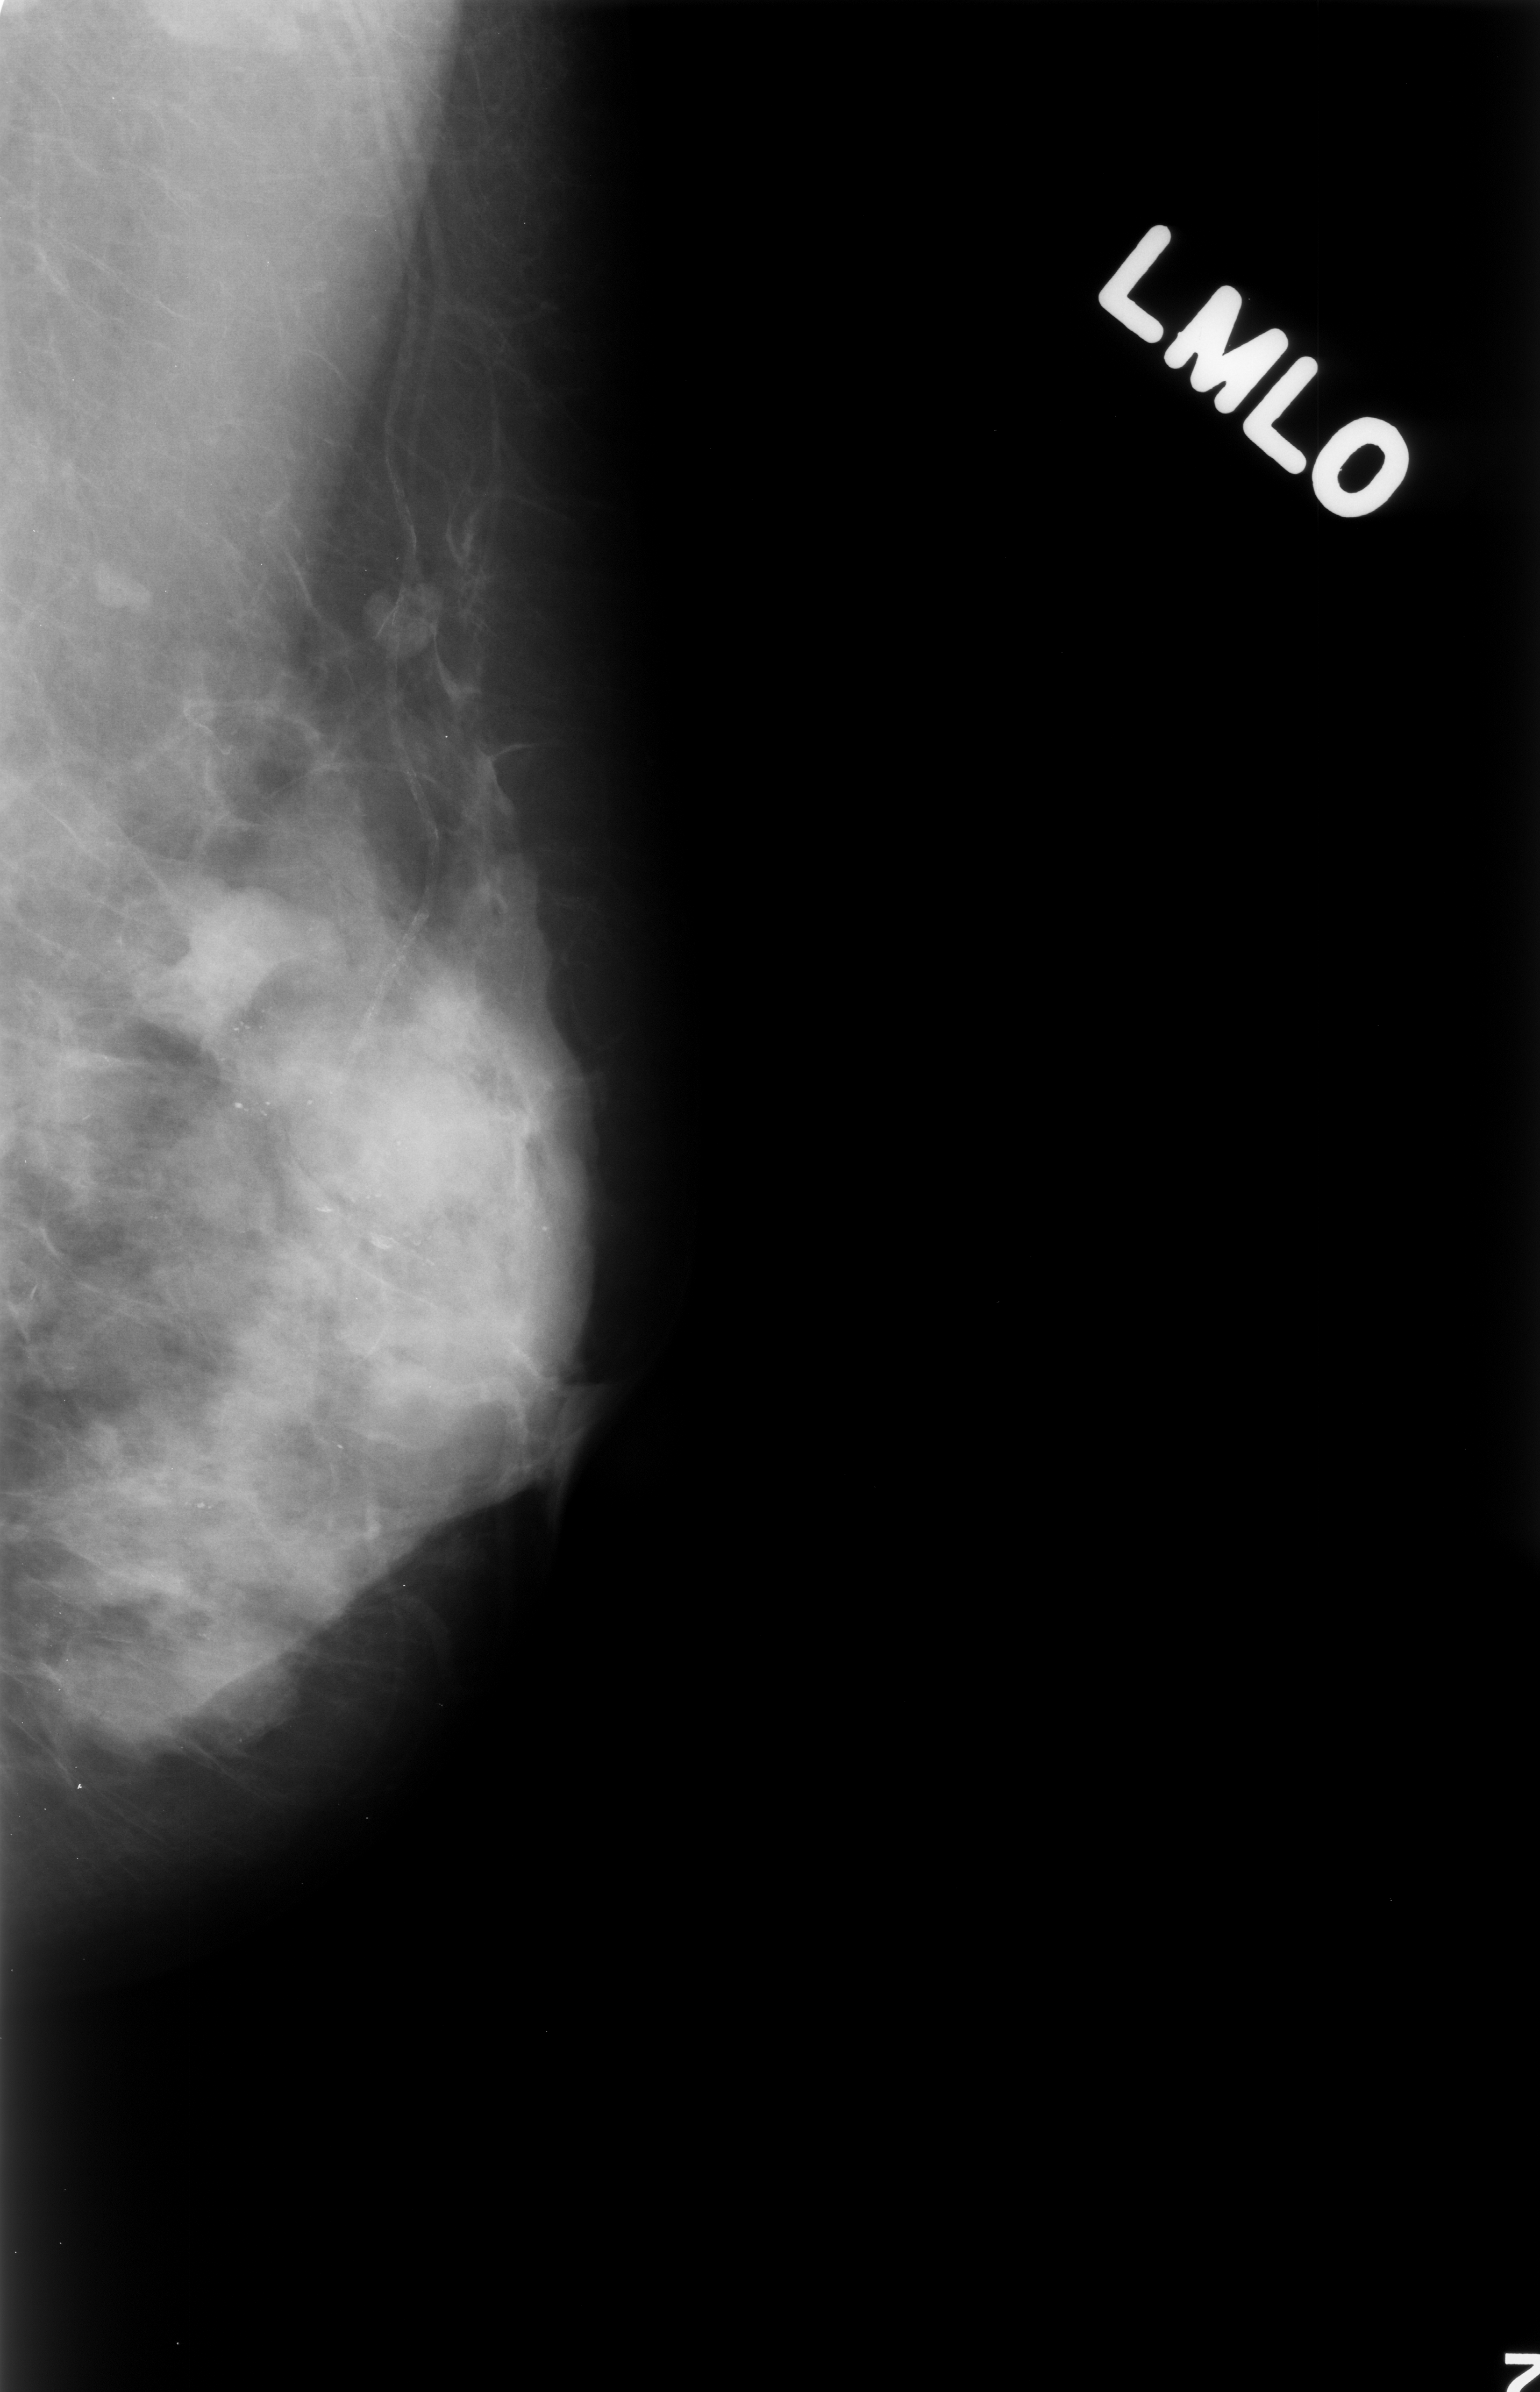
Scanned film-screen mammogram. Left breast. Mediolateral oblique (MLO) view. 1540 × 2392 image matrix.
Marked abnormalities (boxes around the expert regions of interest):
- Finding 1 of 2: mass, shape lobulated, margins obscured; BI-RADS assessment category 3; subtlety rating 5 on a 1 (subtle) to 5 (obvious) scale; pathology result (as recorded, not read from the image): benign: bounding box (x1, y1, x2, y2) in pixels: (149, 880, 312, 1052)
- Finding 2 of 2: mass, shape oval, margins circumscribed; BI-RADS assessment category 3; pathology (as recorded): benign: (325, 1071, 486, 1222)